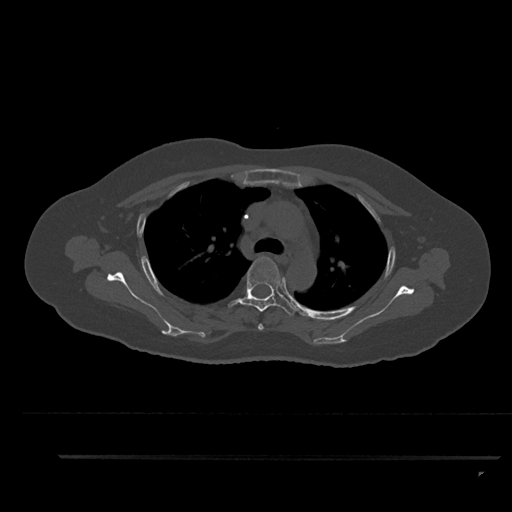
CT including the spine, one axial slice. Slice 648 of 797 in the series (ordered by position). Reconstruction kernel Br40s/3. Bone window (W 1800 / L 400 HU). 0.5 mm slice thickness. 512 × 512 image matrix. Female patient, age 44 years. Case-level facts recorded for this patient, not image findings: primary cancer: renal; vertebrae with lytic lesions (as recorded): L1.
Structures marked on this image (semi-automatic segmentation, software-assisted and operator-edited):
- T3 vertebra: box from (x=258, y=324) to (x=264, y=330) px
- T4 vertebra: (x=228, y=257)–(x=296, y=316)